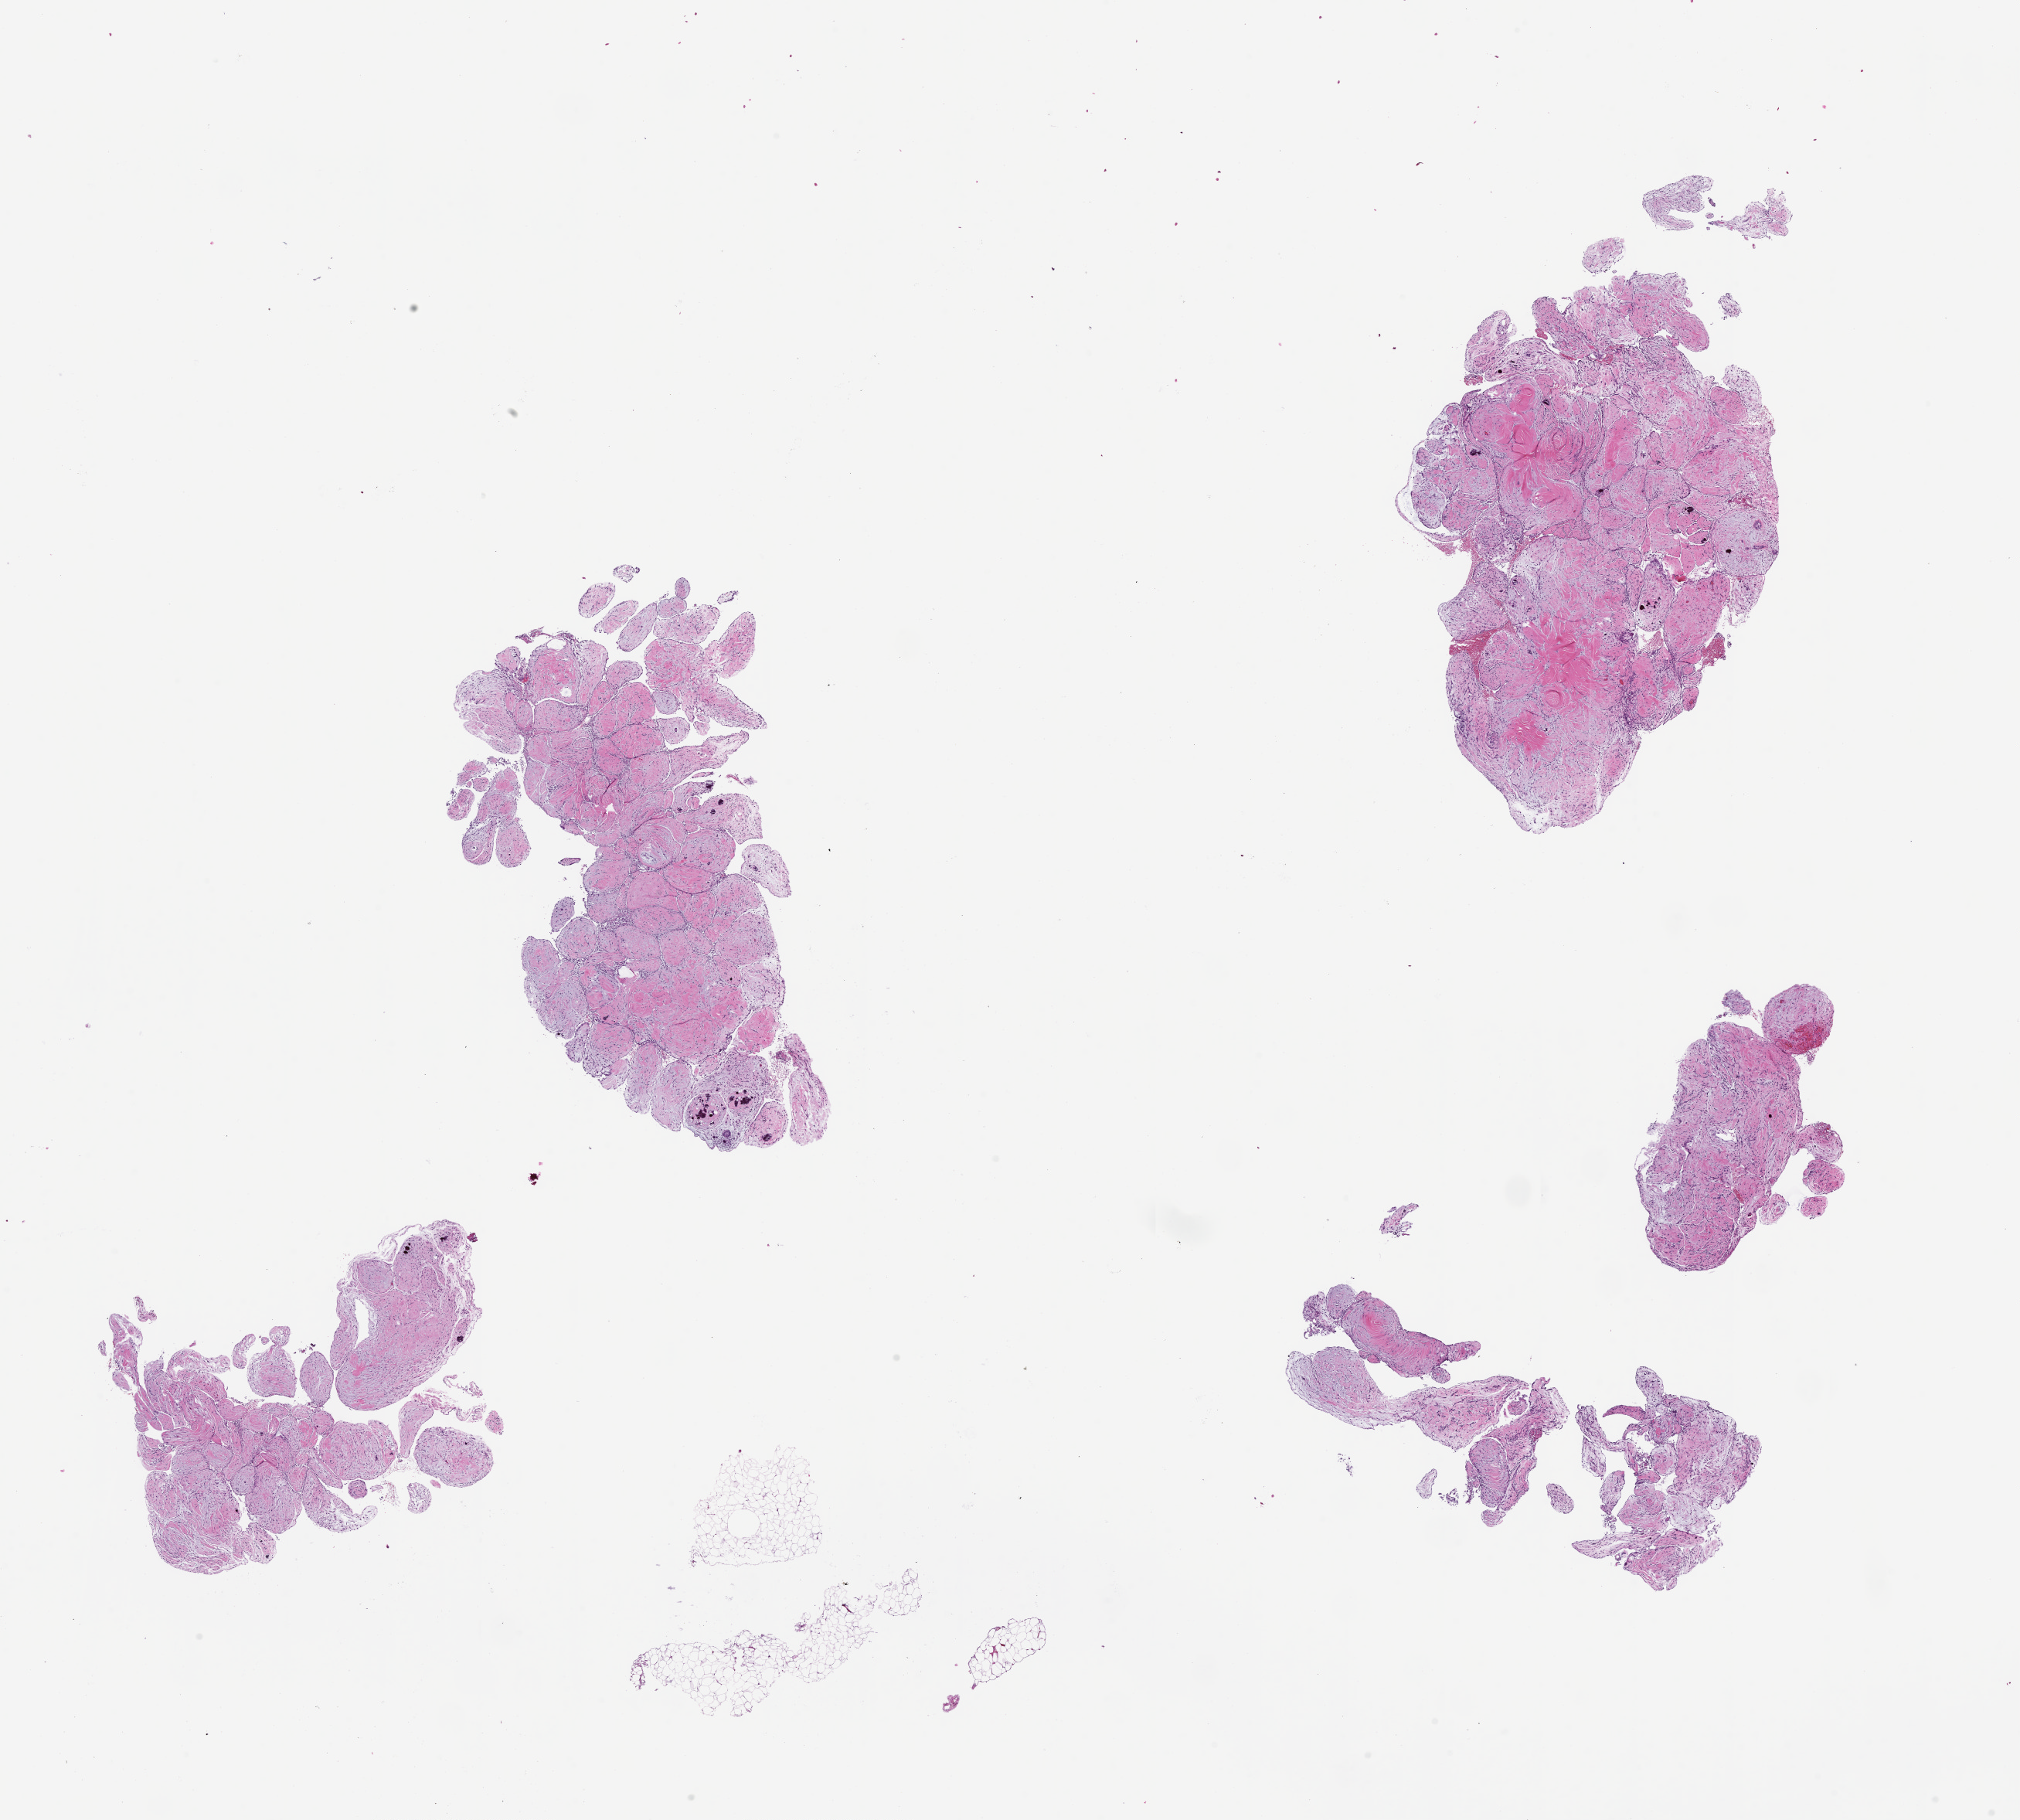
H&E whole-slide image — a low-resolution overview of the entire scanned area, about 21.0 x 19.0 mm; formalin-fixed paraffin-embedded section; collected on treatment. Female patient.
* this section: metastatic tumor tissue
* patient diagnosis (primary): Ovarian Carcinoma